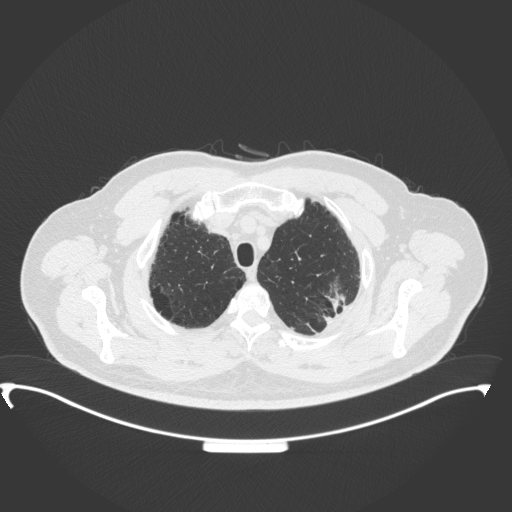
Chest CT, one axial slice; slice 310 of 350 in the series (ordered by position); 120 kVp; lung window (W 1500 / L -600 HU); 1 mm slice thickness; 512 × 512 image matrix, field of view 459 × 459 mm. Male patient, age 64 years. Case-level facts recorded for this patient, not image findings: clinical TNM (as recorded): T1c N1 M1.
Outlined on this slice (rectangle marked by the reading radiologist):
- lung tumour (recorded histology: adenocarcinoma): box from (x=321, y=275) to (x=348, y=311) px